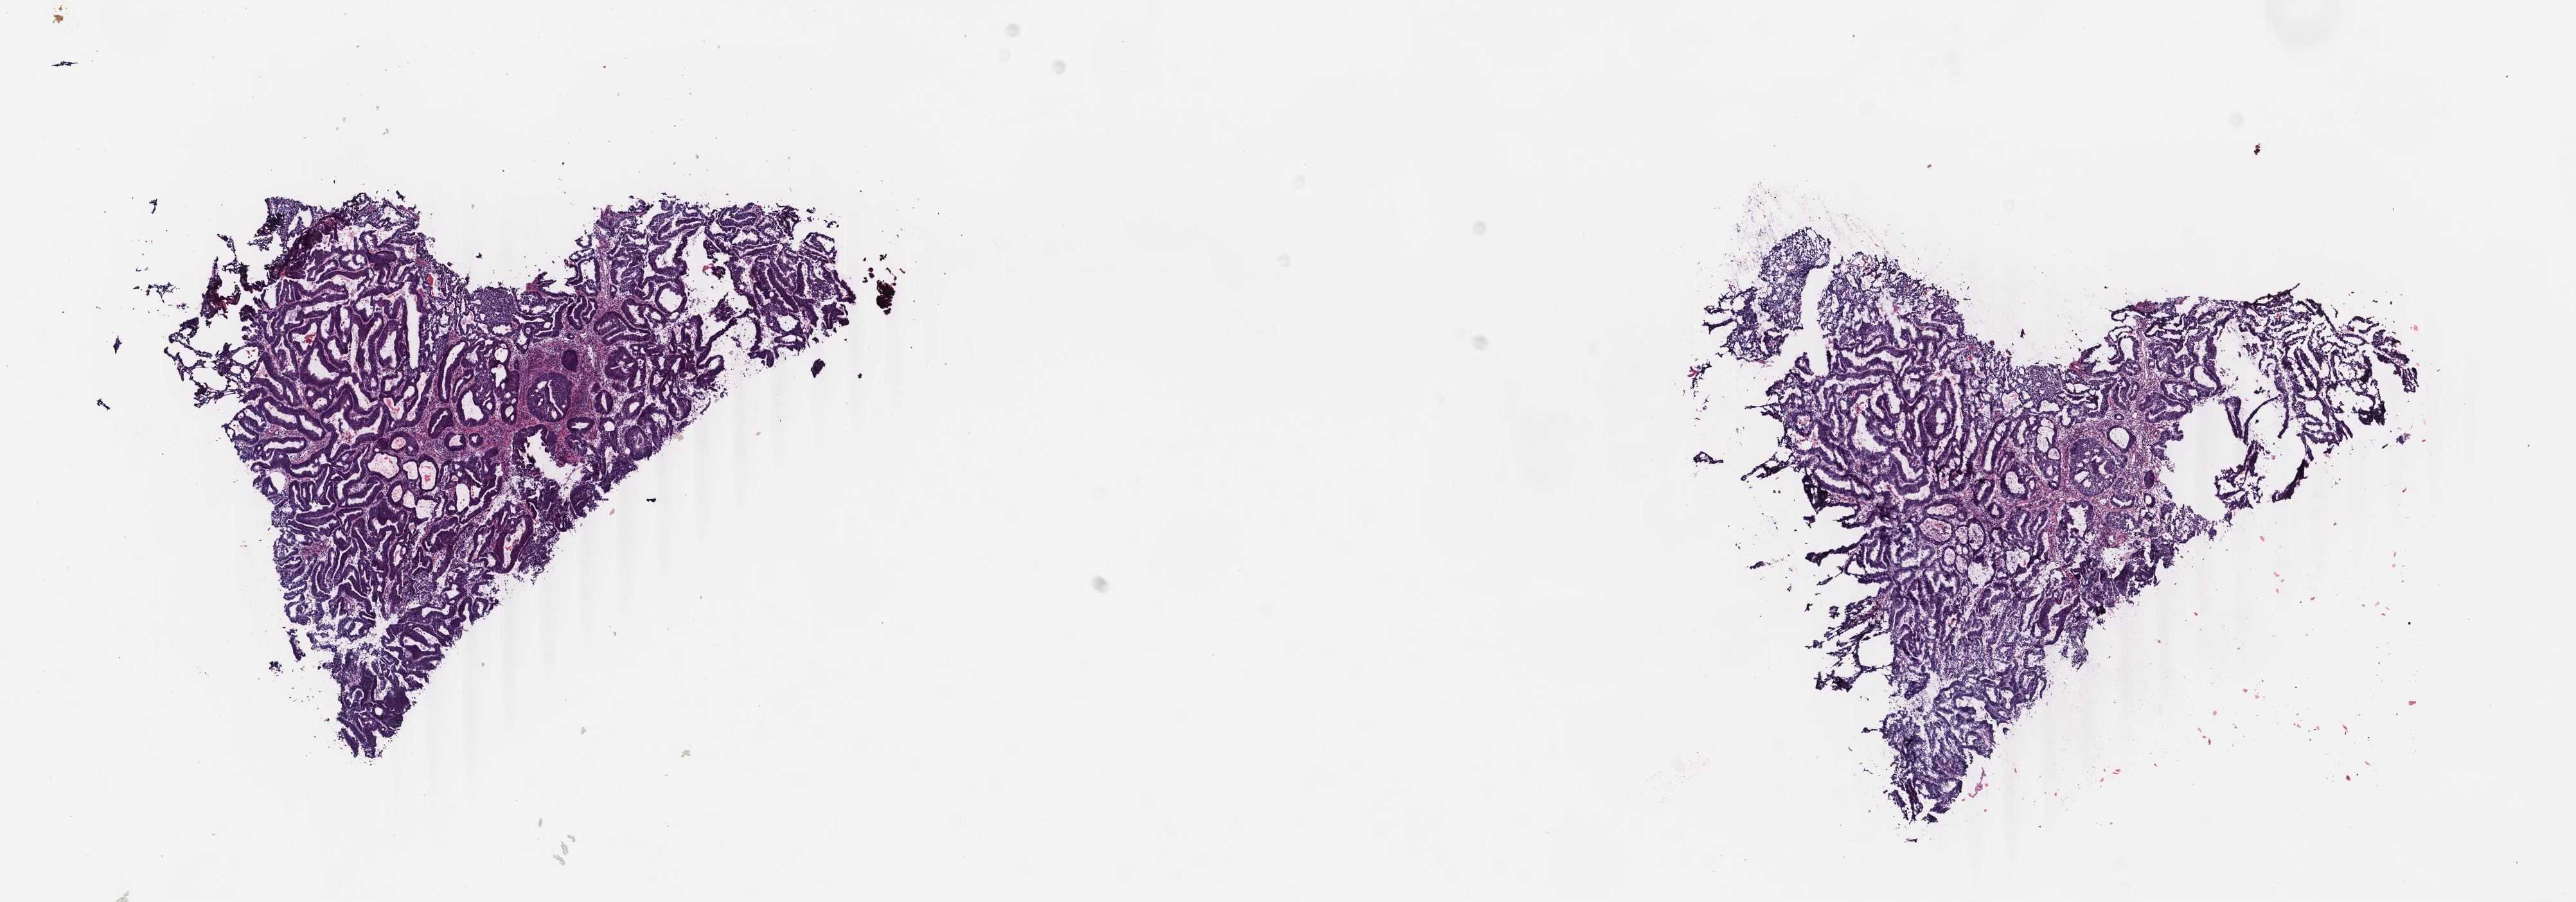
Digitized H&E tissue section (whole slide), low-resolution overview of the scanned area, about 15.9 x 5.6 mm; frozen section from the bottom of the tissue portion; uterus, primary tumour sample. Patient: female, age at initial diagnosis 63 years. Histologic grade: G2 (moderately differentiated). Composition of this section per pathologist review: tumour cells 65%, tumour nuclei 85%, normal cells 10%, stromal cells 5%, necrosis 20%. Infiltration values recorded for this section: lymphocyte infiltration 10%, monocyte infiltration 0%, neutrophil infiltration 10%.
- FIGO stage: IA
- lymph nodes positive (case pathology): 0 of 16 examined
- histologic diagnosis: Endometrioid adenocarcinoma, NOS (endometrium)